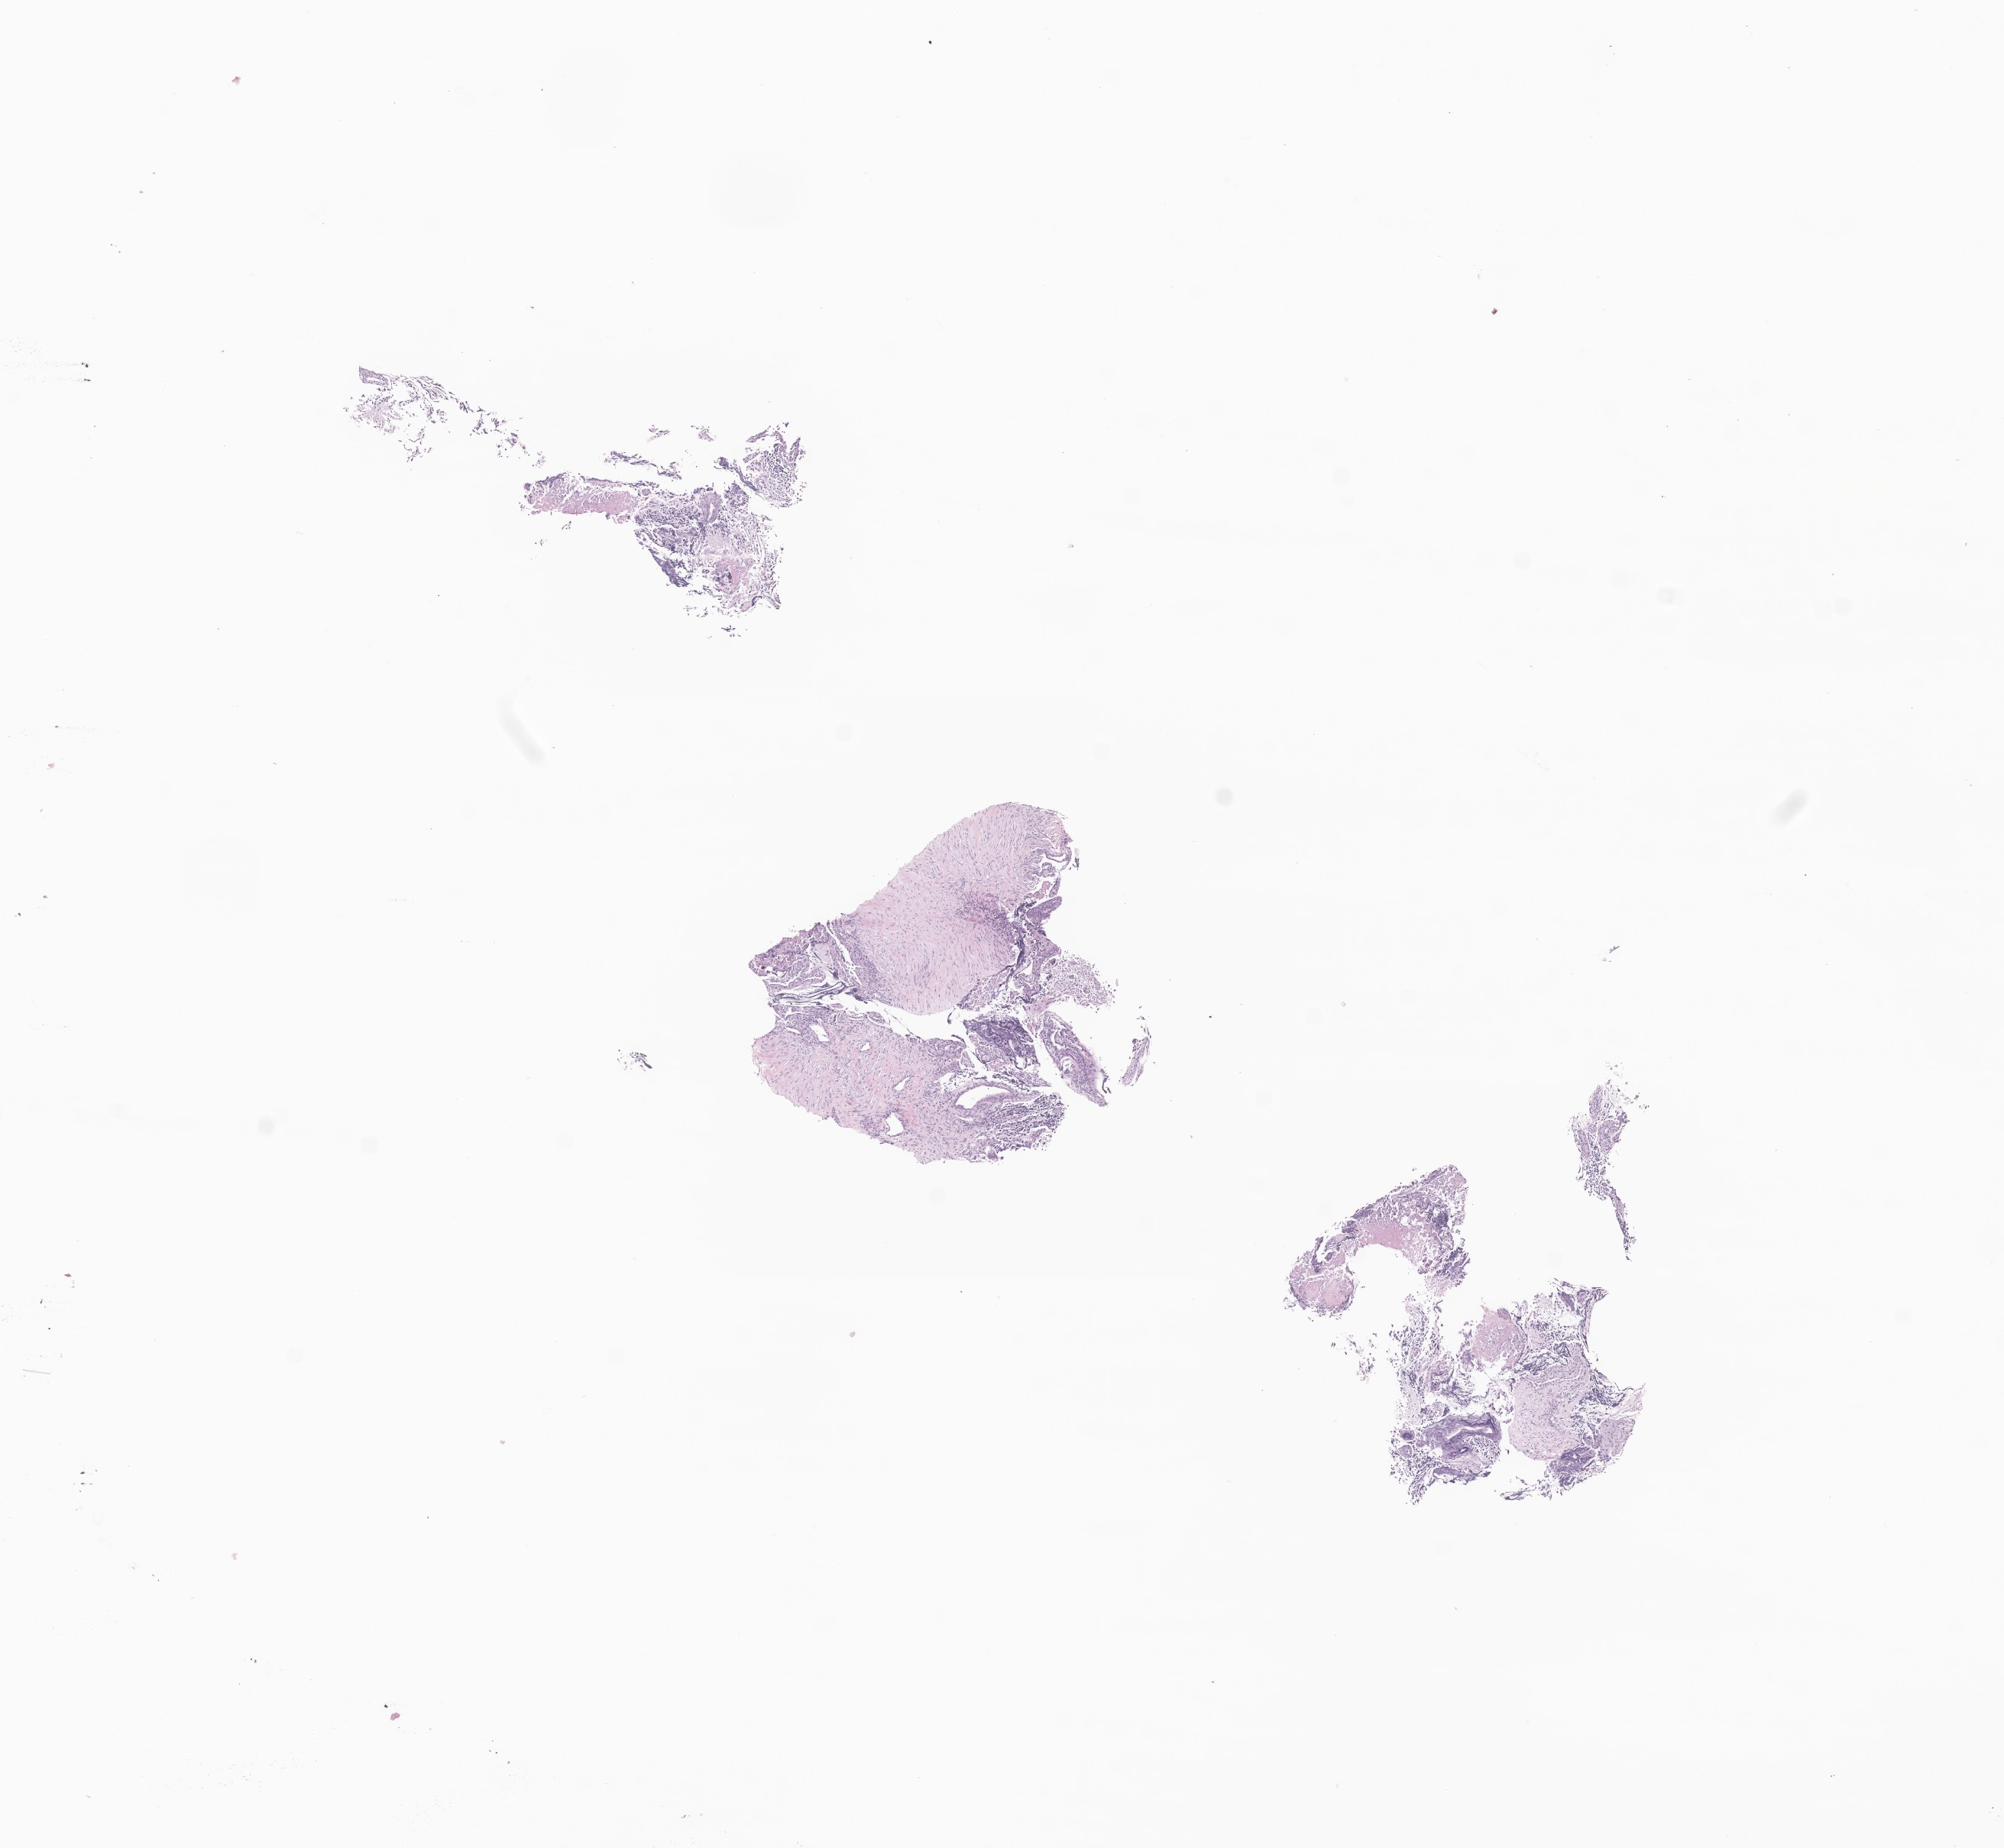
Digitized haematoxylin and eosin-stained section of tumor tissue from the abdomen, shown as a low-resolution overview of the whole scanned area (about 11.1 x 10.2 mm), FFPE section. Female patient, age 264 days.
Diagnosis: Neuroblastoma, NOS.